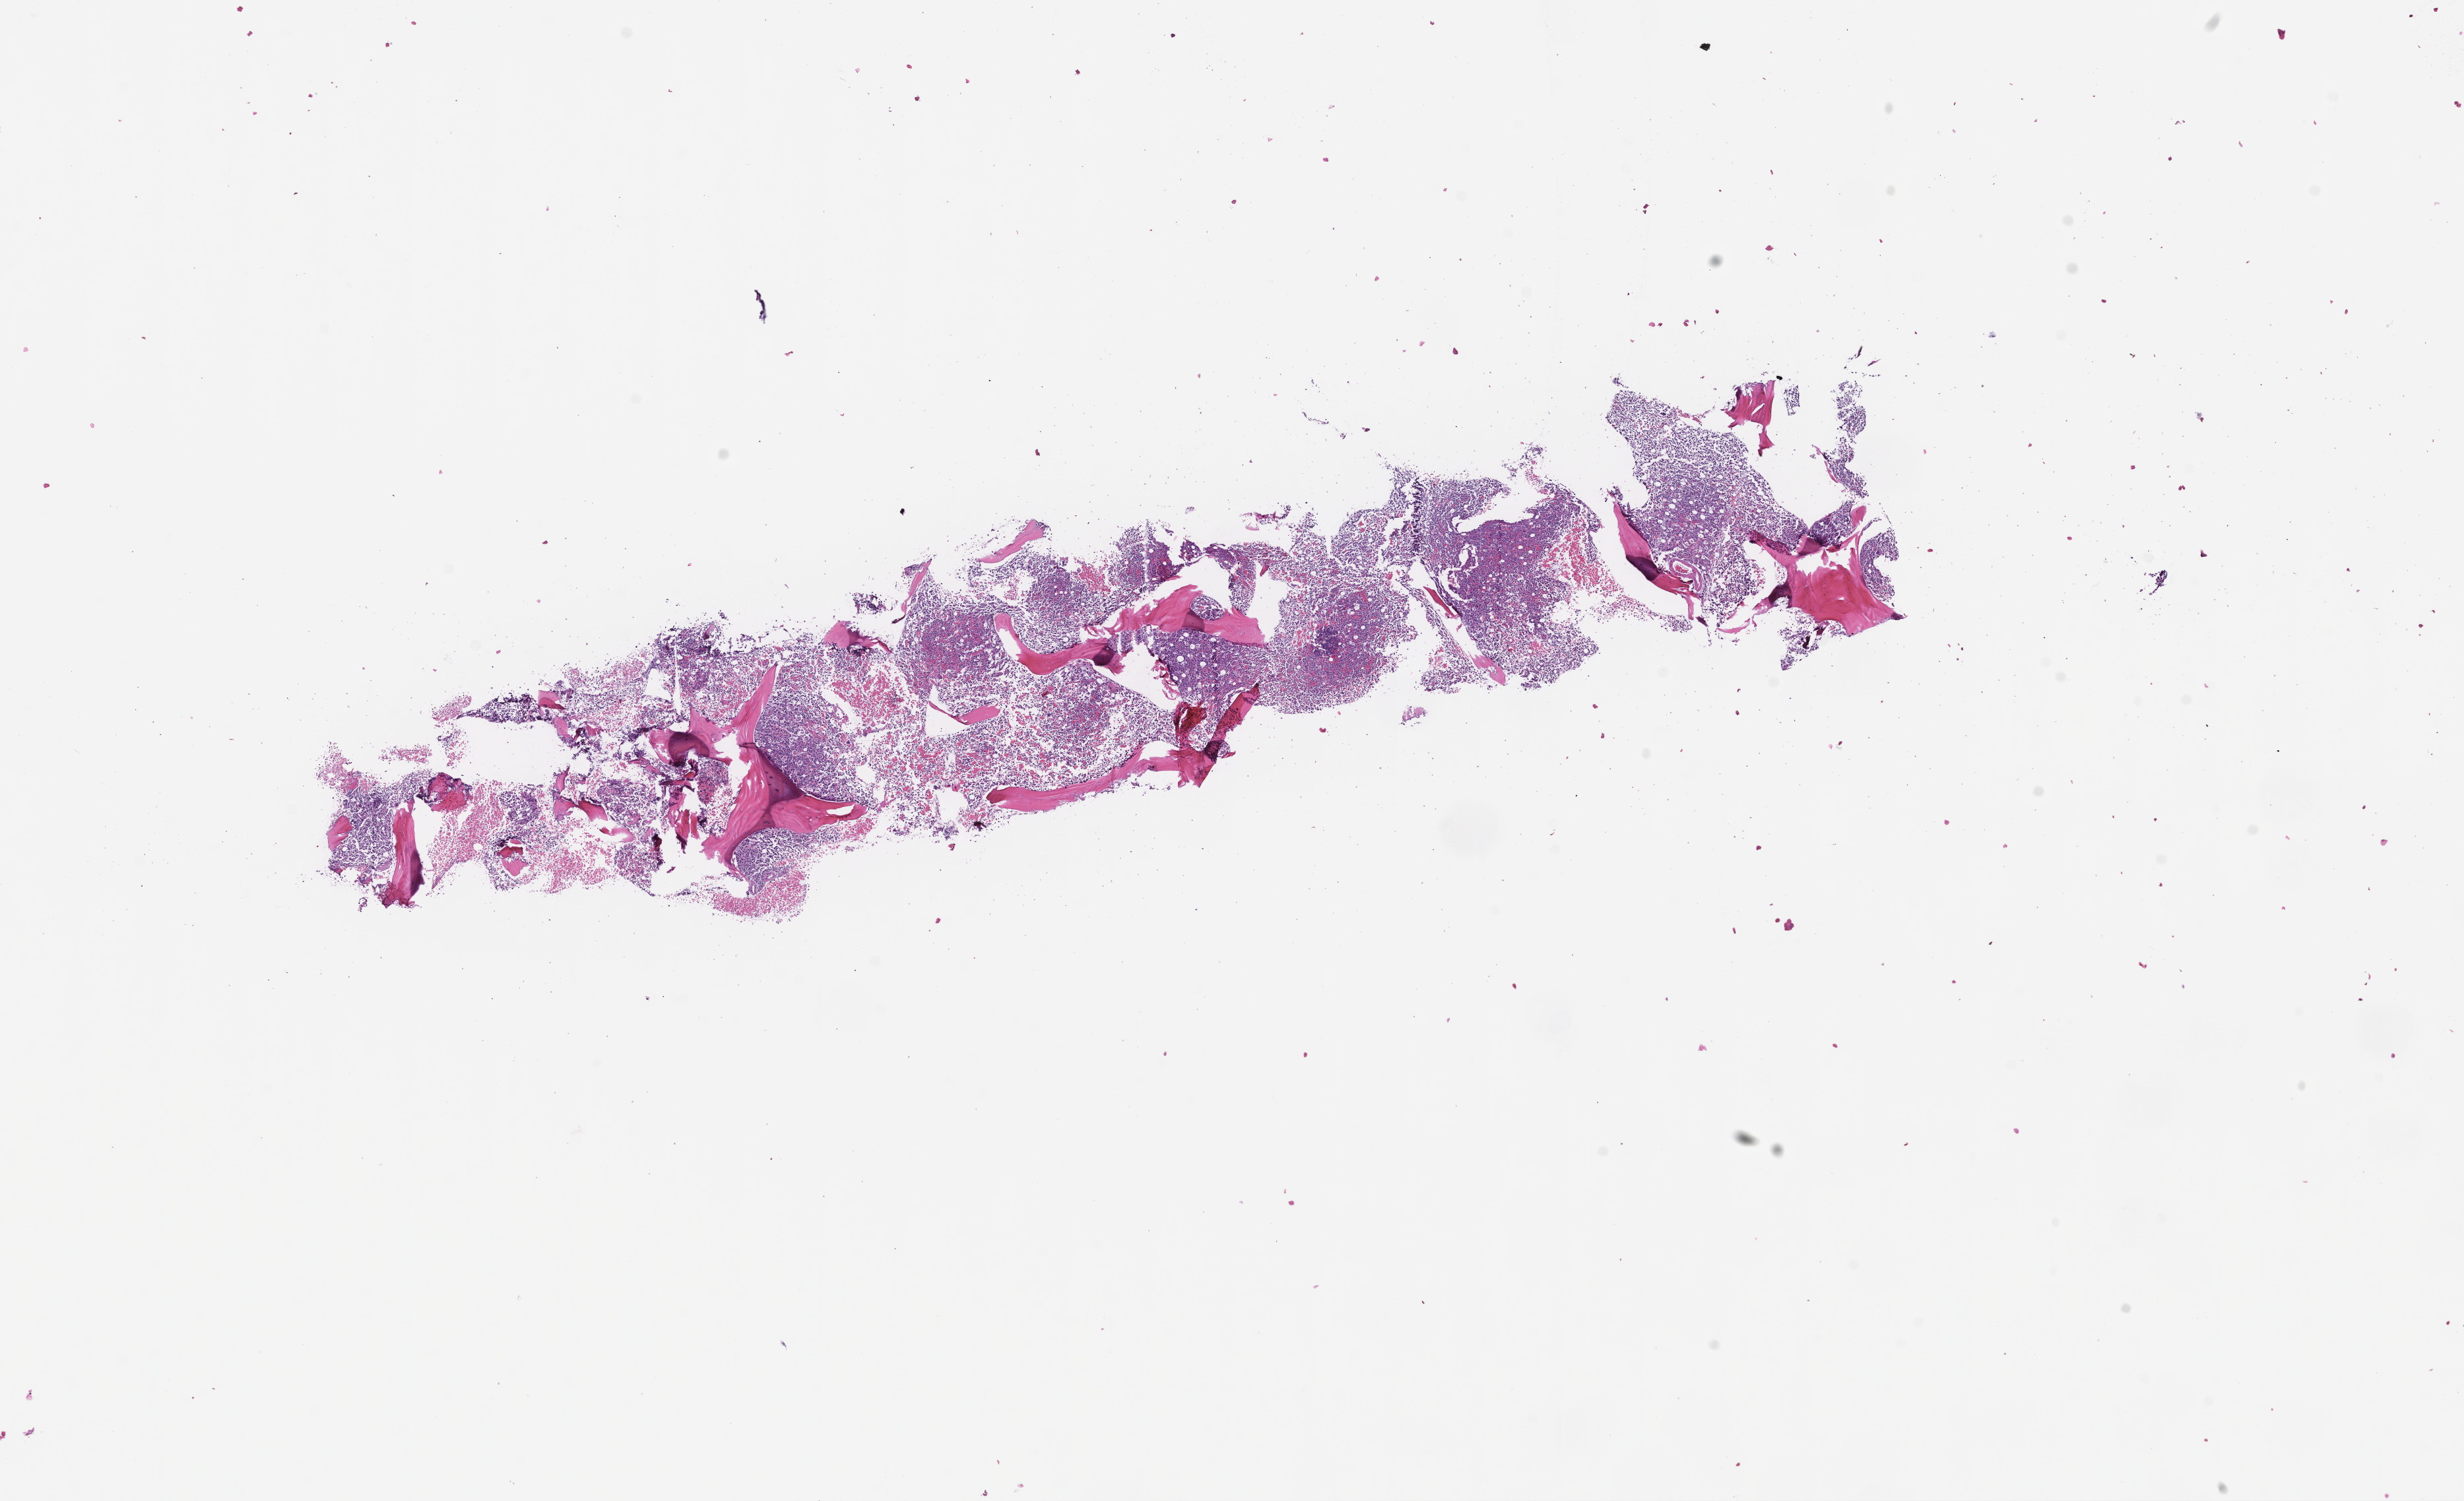
Digitized haematoxylin and eosin-stained section — whole scanned area (about 15.1 x 9.2 mm) shown as a low-resolution overview, formalin-fixed, paraffin-embedded (FFPE) tissue, site: bone marrow, collected at baseline (before treatment). Patient sex: female.
This section: primary tumor. Diagnosis: Acute Myeloid Leukemia Not Otherwise Specified.